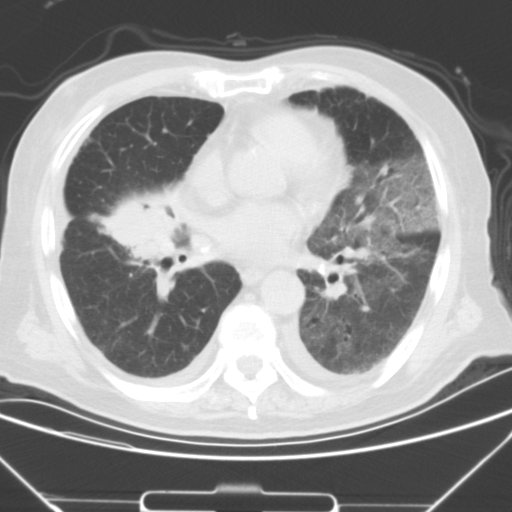
Chest CT, one axial slice; position 15 of 43 along the scan axis; lung window (W 1500 / L -600 HU); 5 mm slice thickness; 512 × 512 image matrix, field of view 343 × 343 mm. Patient: male, 85 years. Case-level facts recorded for this patient, not image findings: clinical TNM (as recorded): T4 N3 M2.
Annotated regions visible in this slice (rectangle marked by the reading radiologist):
- lung tumour (recorded histology: squamous cell carcinoma): bounding box [x1, y1, x2, y2] px = [103, 189, 189, 292]